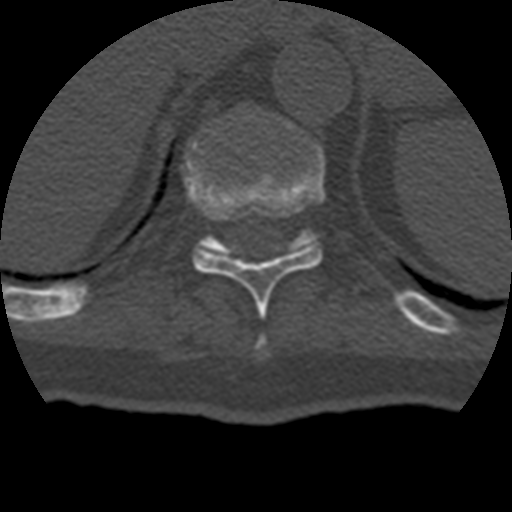
CT including the spine, one axial slice. Position 212 of 399 along the scan axis. Reconstruction kernel STANDARD. Bone window (W 1800 / L 400 HU). 512 × 512 image matrix, field of view 160 × 160 mm. Patient age 69 years. From the clinical record (not read from this slice): primary cancer: prostate.
Structures marked on this image (semi-automatic segmentation, software-assisted and operator-edited):
- T10 vertebra: bounding box (x1, y1, x2, y2) in pixels: (187, 143, 325, 315)
- T11 vertebra: (201, 110, 318, 249)
- T9 vertebra: (259, 341, 264, 346)